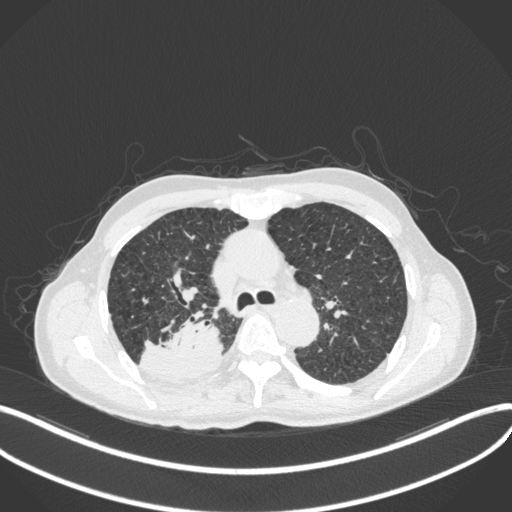
Chest CT, one axial slice; position 306 of 423 along the scan axis; 120 kVp; lung window (W 1500 / L -600 HU); 1 mm slice thickness; 512 × 512 image matrix, field of view 400 × 400 mm. Patient: male, 79 years. Case-level facts recorded for this patient, not image findings: clinical TNM (as recorded): T3 N0 M0.
Outlined on this slice (bounding box drawn by a radiologist):
- lung tumour (recorded histology: adenocarcinoma): bounding box <137,319,223,384> (left, top, right, bottom; pixels)